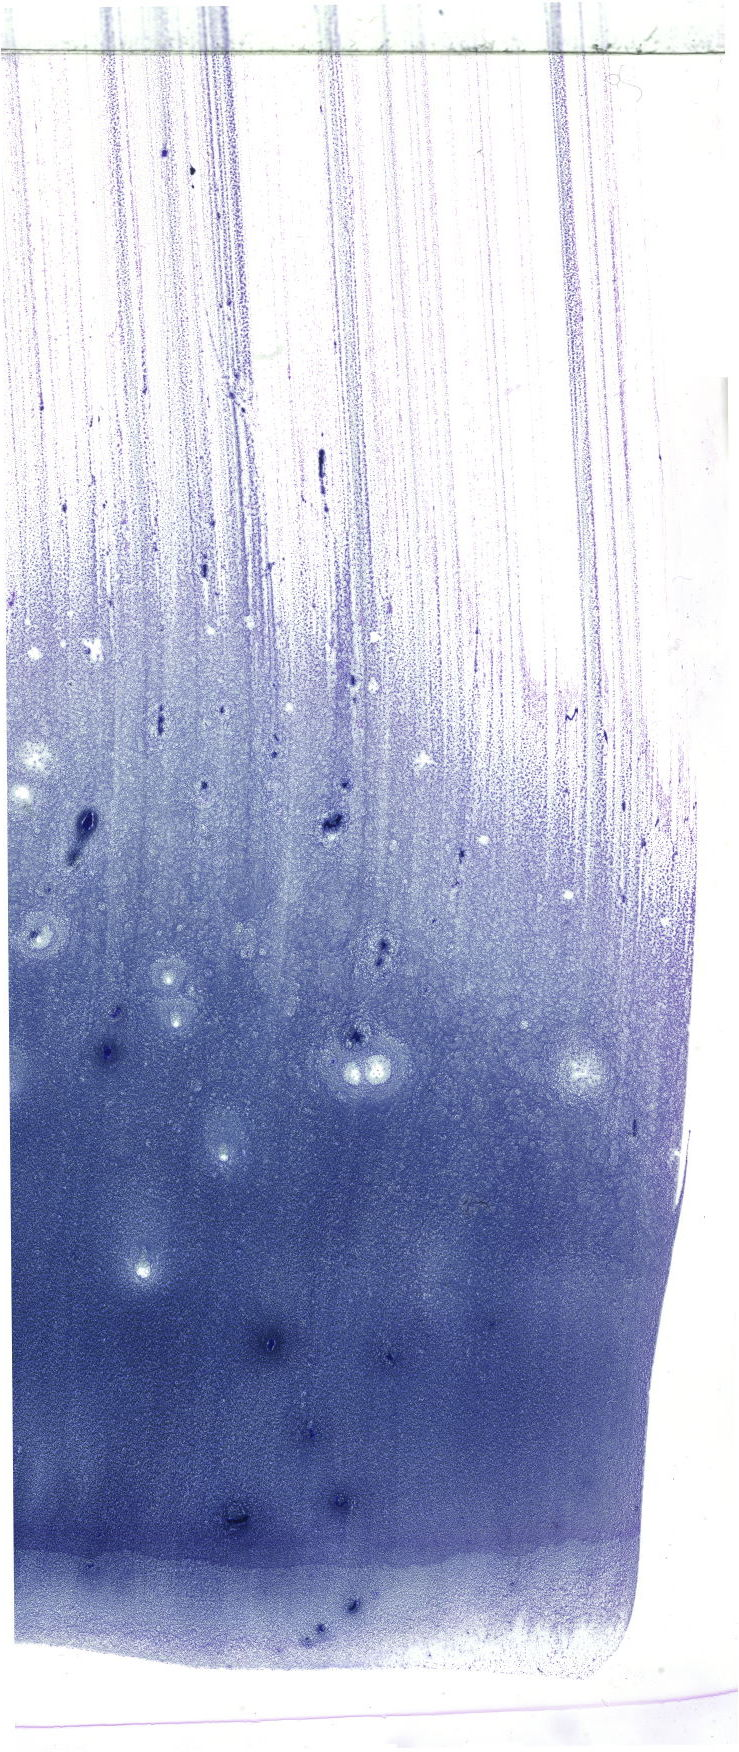
May-Grünwald–Giemsa-stained marrow aspirate smear (whole slide) — a low-resolution overview of the entire scanned area, about 20.9 x 49.7 mm. Male patient.
Diagnosis: B Acute Lymphoblastic Leukemia.